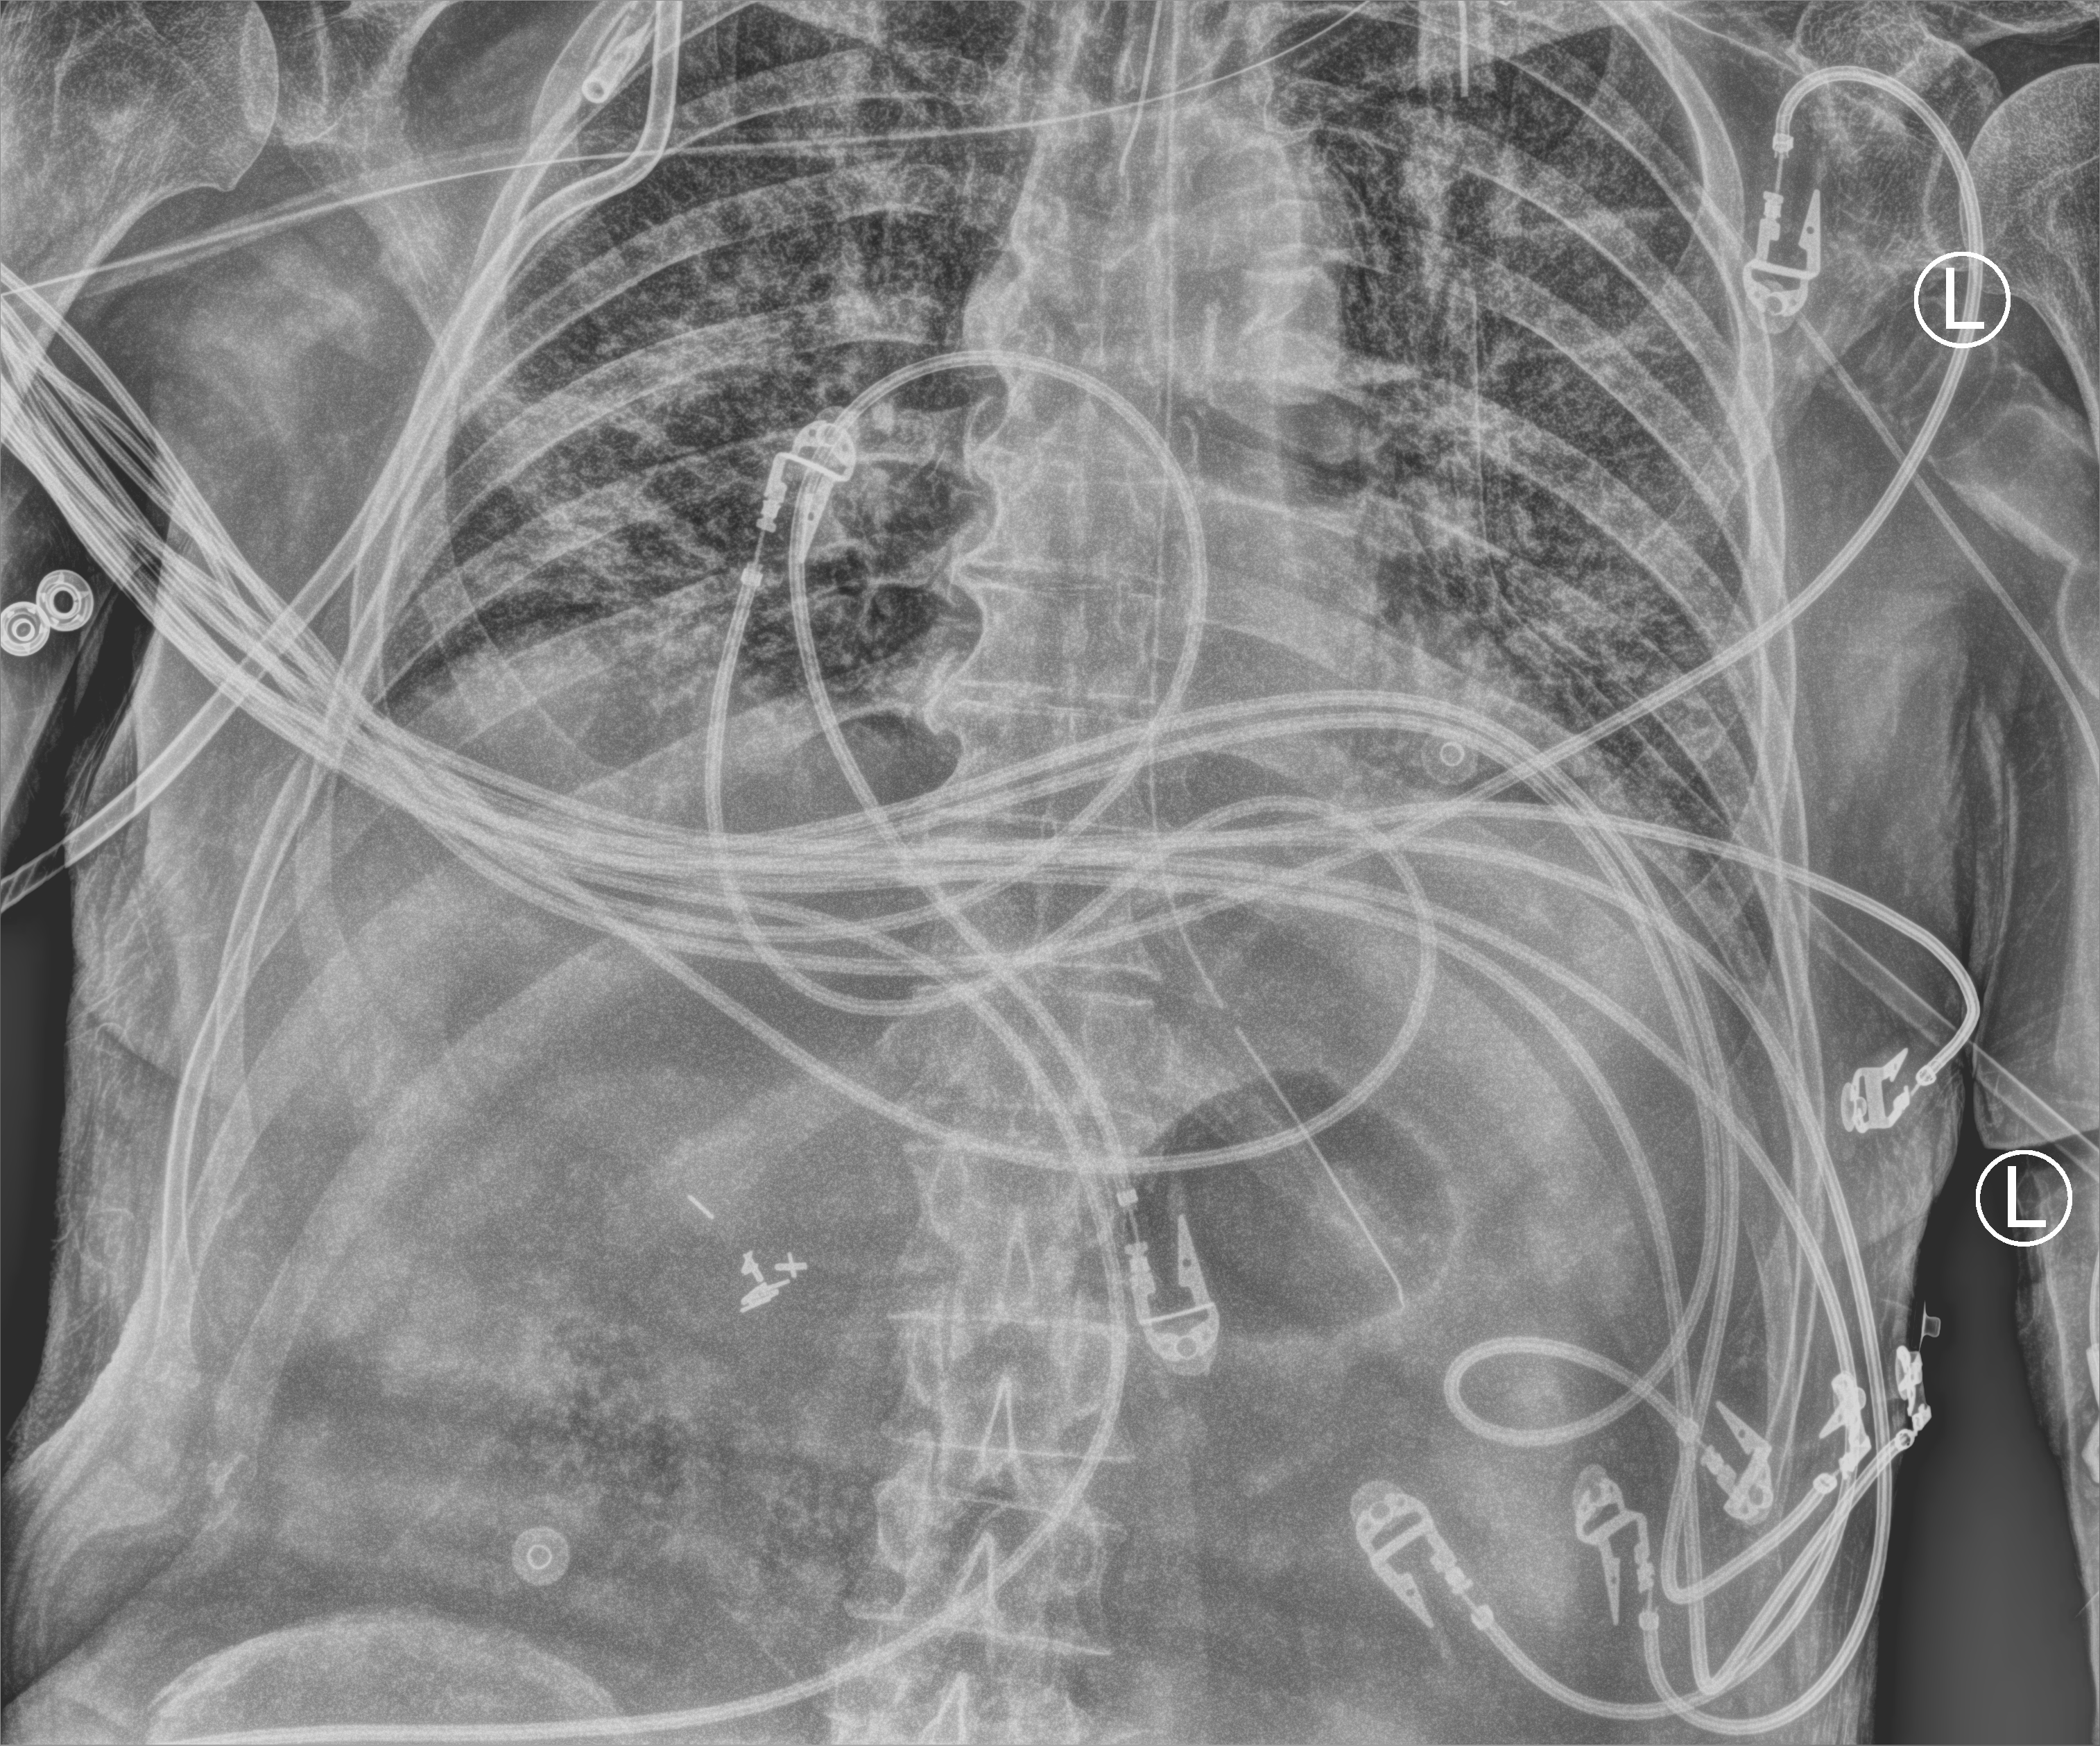
Bedside chest radiograph (computed radiography); anteroposterior (AP) projection. Patient hospitalised with COVID-19; male, aged 75–90 years.
Admission-level facts for this patient (not findings on this image; timing relative to this image not recorded):
- mechanically ventilated during this hospital stay: yes
- admitted to intensive care during this hospital stay: yes
- length of hospital stay: 23 days